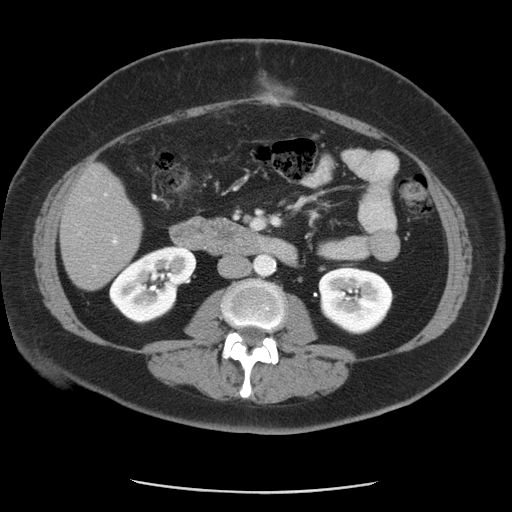
Contrast-enhanced abdominal CT, one axial slice; 120 kVp; intravenous contrast given; soft-tissue window (W 400 / L 40 HU); 5 mm slice thickness; 512 × 512 image matrix, field of view 380 × 380 mm. Female patient, age 52 years. From the clinical record (not read from this slice): diagnosis: colorectal cancer liver metastases, imaged before liver resection; multiple liver metastases: yes; largest metastasis: 2.5 cm; disease in both lobes: yes.
Structures marked on this image (manually delineated by an expert):
- liver: bounding box (x1, y1, x2, y2) in pixels: (60, 165, 143, 290)
- planned liver remnant (the part of the liver to remain after resection): (60, 193, 135, 290)
- portal vein (with intrahepatic branches): (77, 191, 120, 272)